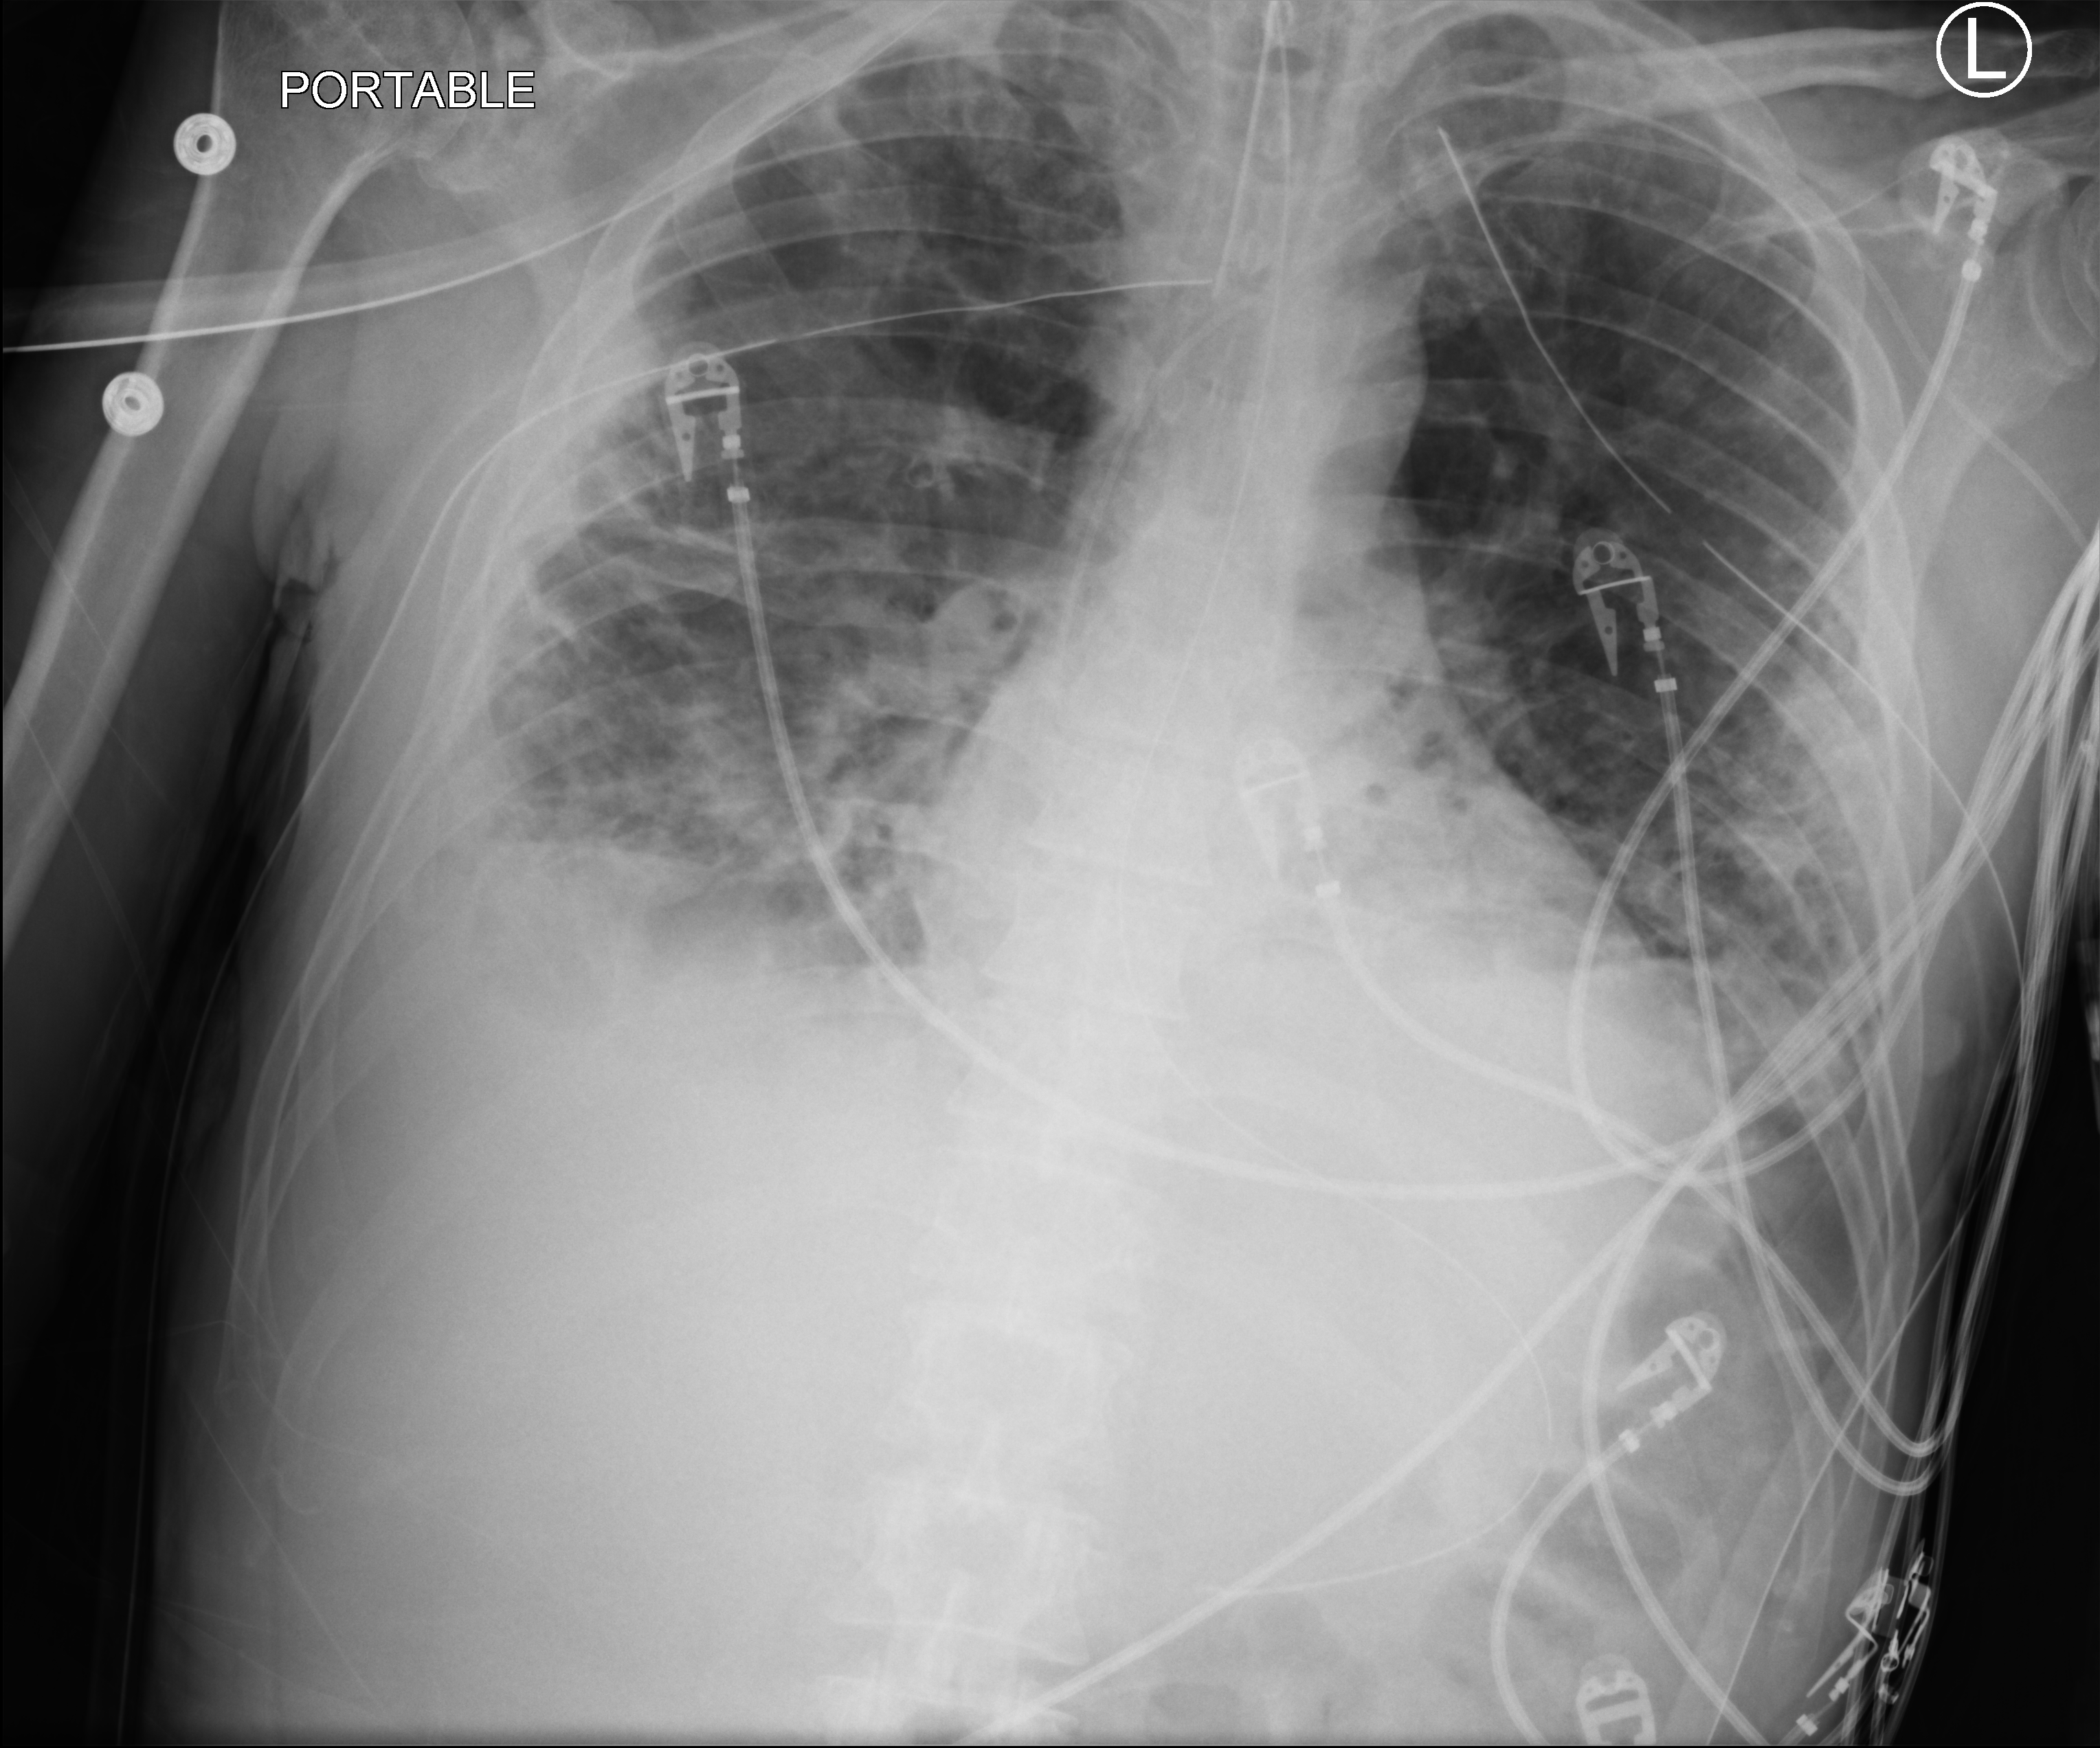
Bedside chest radiograph (computed radiography); anteroposterior (AP) projection. Patient hospitalised with COVID-19; male, aged 18–59 years.
Admission-level facts for this patient (not findings on this image; timing relative to this image not recorded): admitted to intensive care during this hospital stay: yes; length of hospital stay: 96 days.